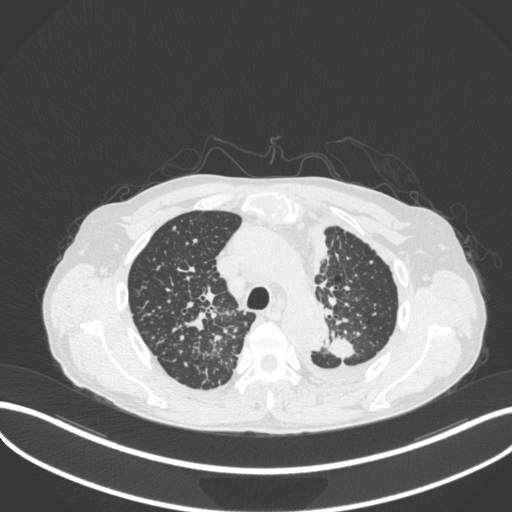
Chest CT, one axial slice. 120 kVp. Lung window (W 1500 / L -600 HU). 1 mm slice thickness. 512 × 512 image matrix, field of view 400 × 400 mm. Patient: male, 58 years. Case-level facts recorded for this patient, not image findings: clinical TNM (as recorded): T1c N3 M1.
Outlined on this slice (bounding box drawn by a radiologist):
- lung tumour (recorded histology: adenocarcinoma): bounding box [x1, y1, x2, y2] px = [324, 333, 359, 361]